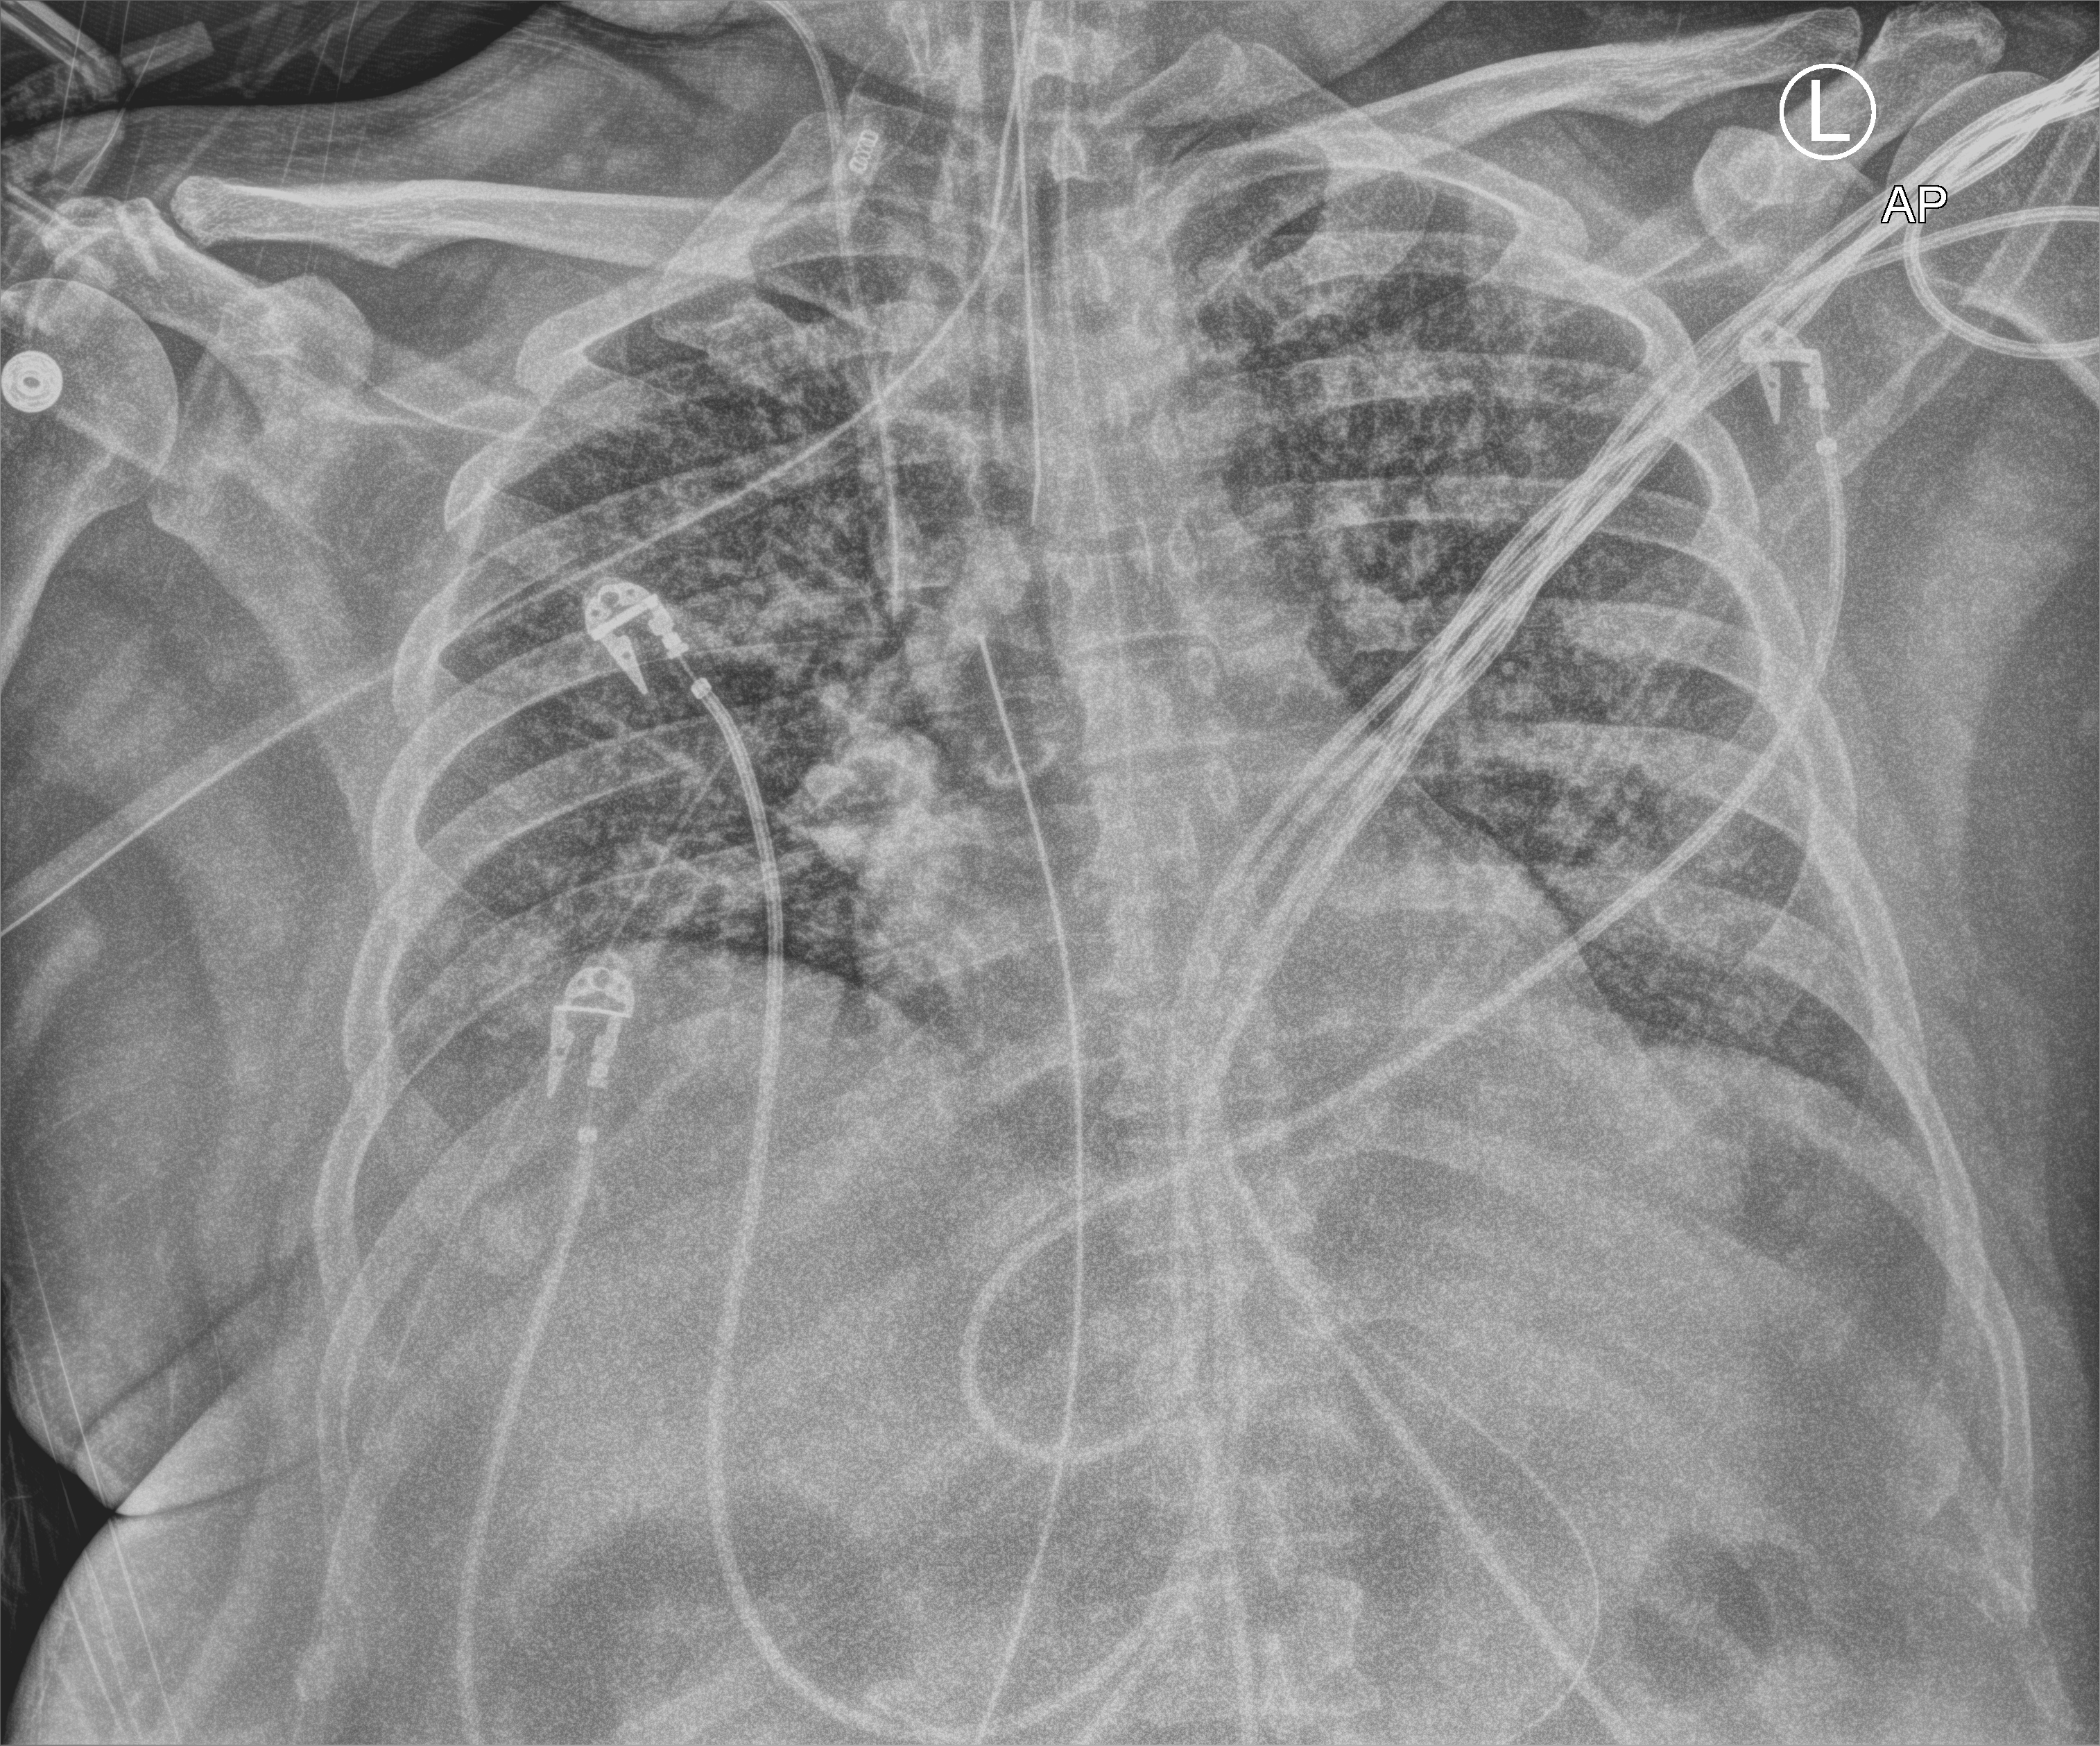
Chest X-ray (portable), anteroposterior (AP) projection. Male patient hospitalised with COVID-19, age 18–59 years.
Admission-level facts for this patient (not findings on this image; timing relative to this image not recorded):
- chronic kidney disease (admission record): no